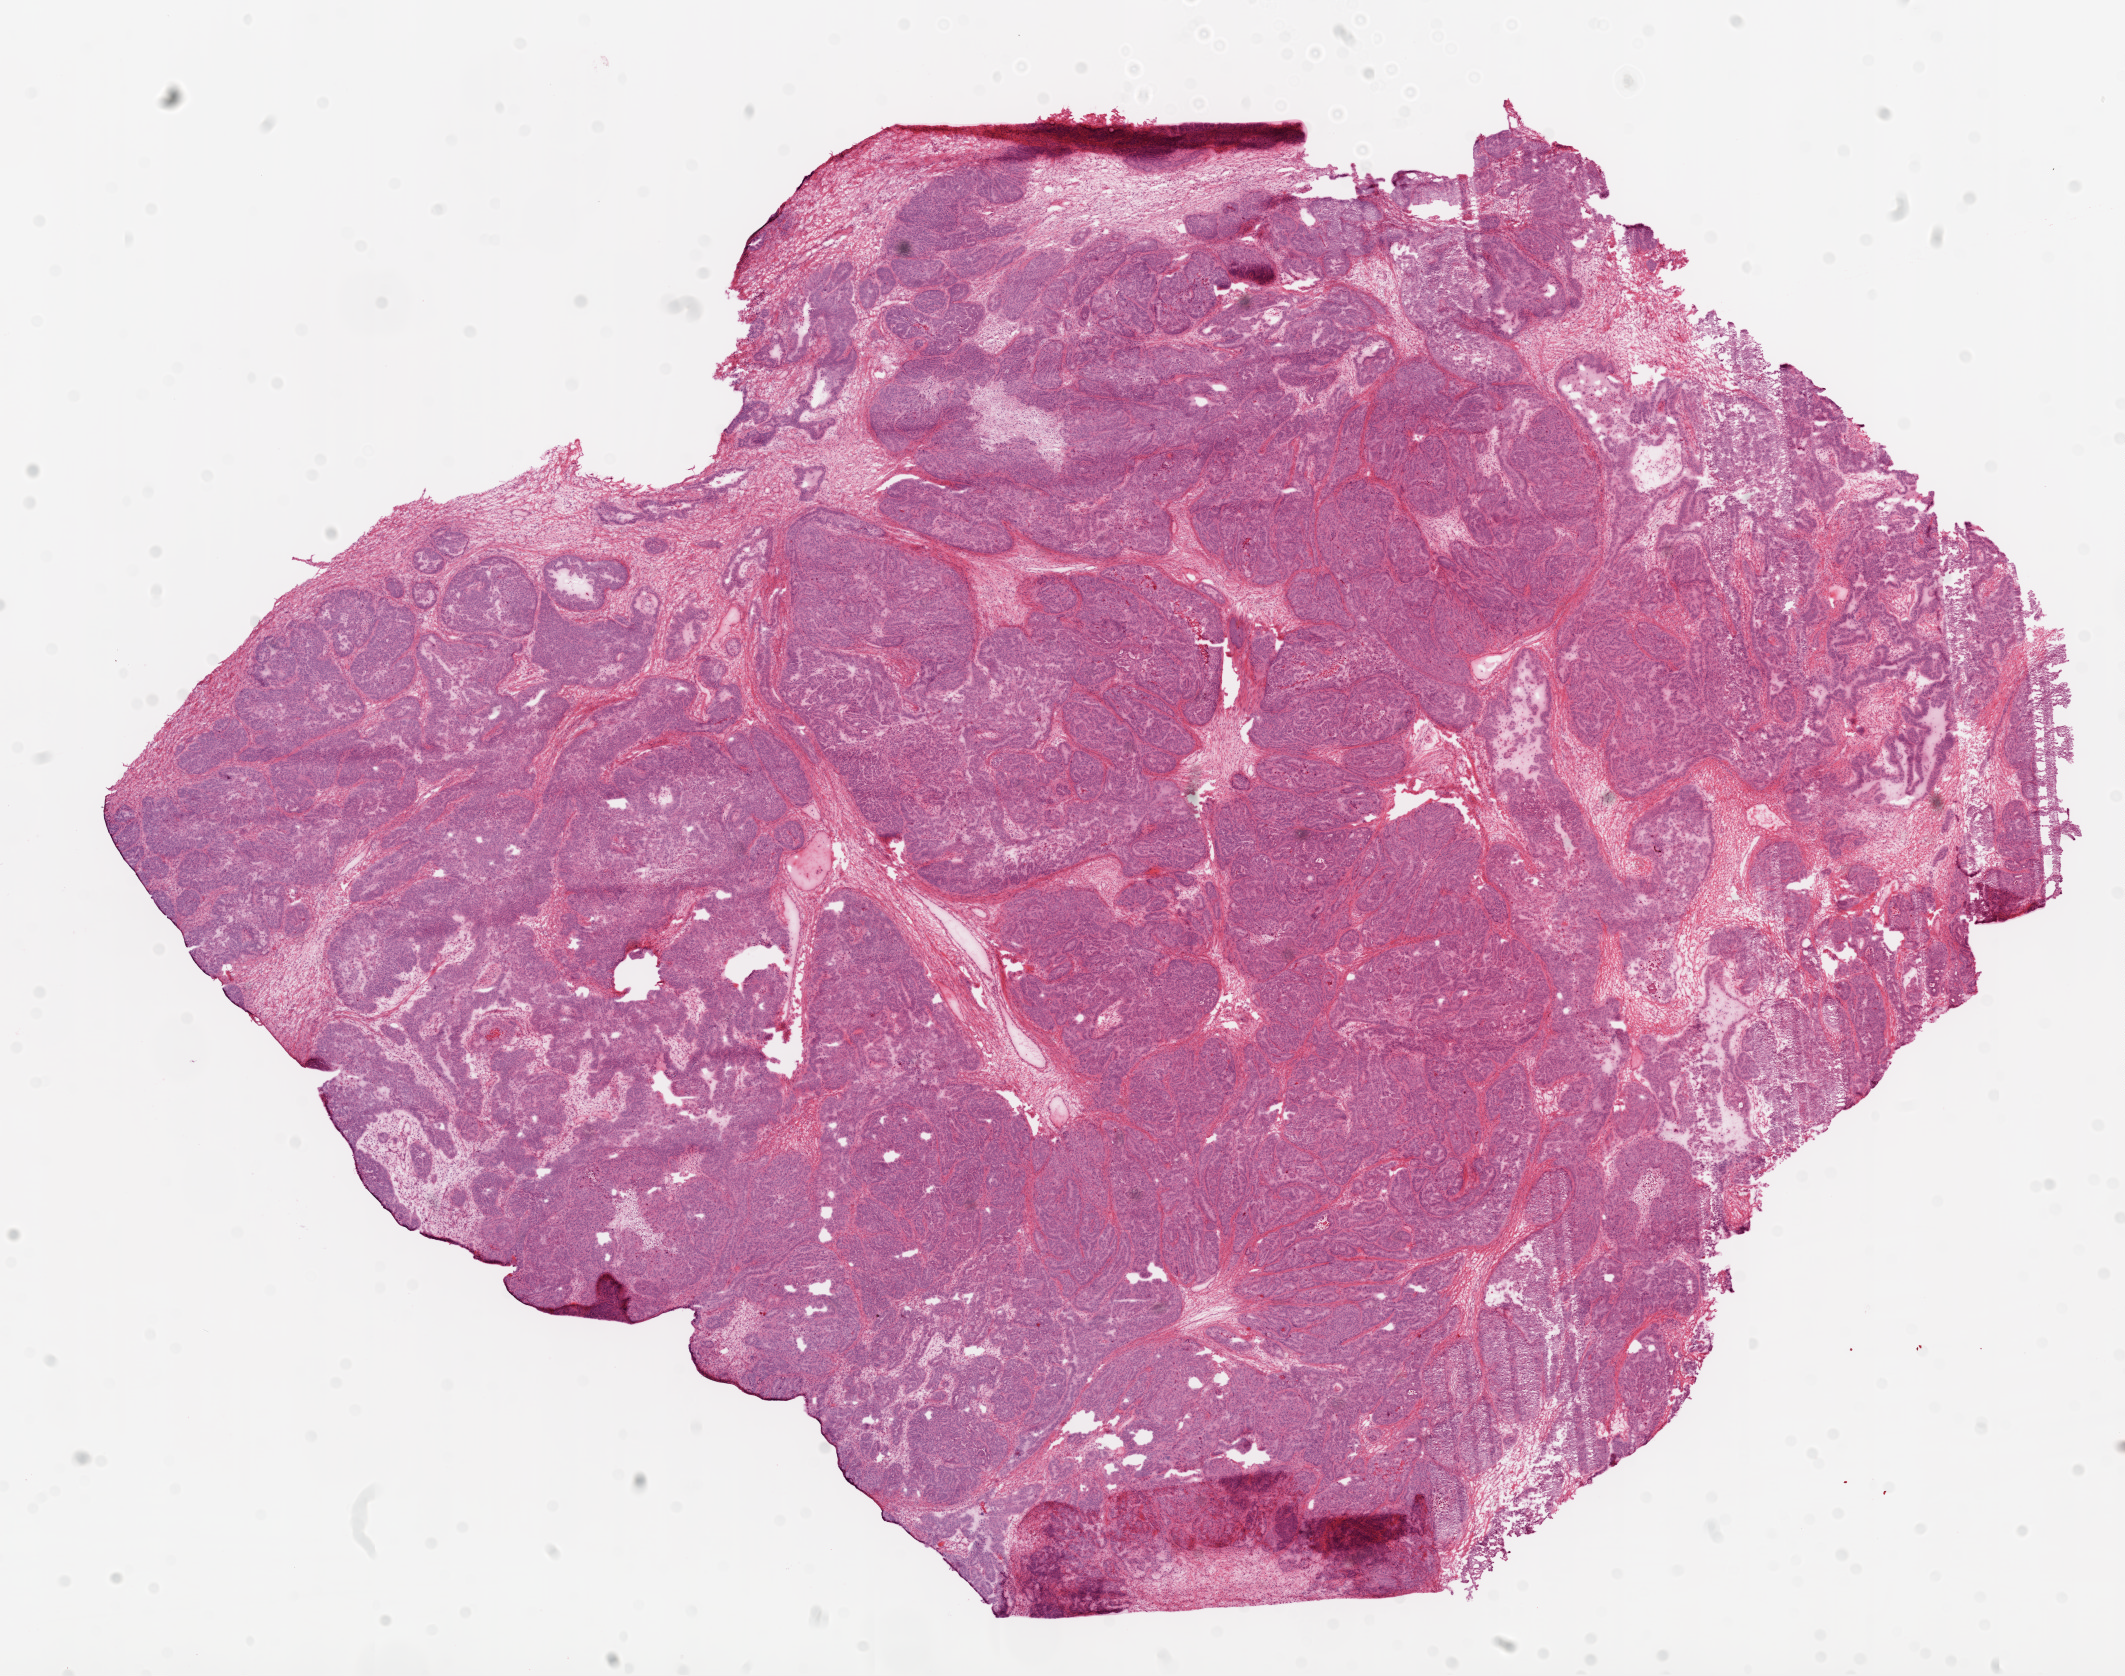
Digitized Hematoxylin and eosin (H&E) stained tissue section (whole slide), shown as a low-resolution overview of the whole scanned area (about 17.1 x 13.4 mm, acquisition: 20x scan); frozen section from the top of the tissue portion; sample: primary tumour, ovary. Female patient; age at initial diagnosis 76 years. Histologic grade: G3 (poorly differentiated). Slide review estimates, as recorded: tumour cells 89%, tumour nuclei 90%, normal cells 0%, stromal cells 10%, necrosis 1%.
FIGO stage: IIIC. Diagnosis: Serous cystadenocarcinoma, NOS.